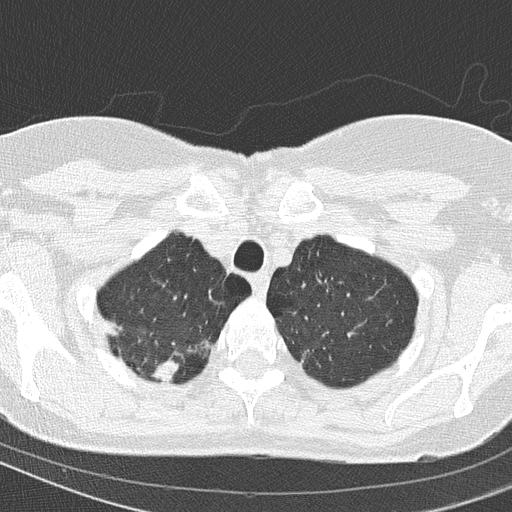
Axial slice from a low-dose chest CT screening exam. Baseline screening round. Lung window (W 1500 / L -600 HU). 120 kVp. Slice 21 of 154 in the series. Female, age 67 years at enrolment. Current smoker at enrolment.
Lesion marked by an expert reader, bounding box [x1, y1, x2, y2] px = [128, 342, 190, 391]. Reader record for this screening exam (exam-level; its link to the box is not recorded): non-calcified nodule or mass ≥4 mm, right upper lobe, 15 × 14 mm, spiculated (stellate) margins, soft tissue attenuation. Participant outcome: lung cancer diagnosed 63 days after this screen — adenocarcinoma, NOS, right upper lobe, moderately differentiated (G2), stage IA (AJCC 6th edition), 14 mm at pathology.